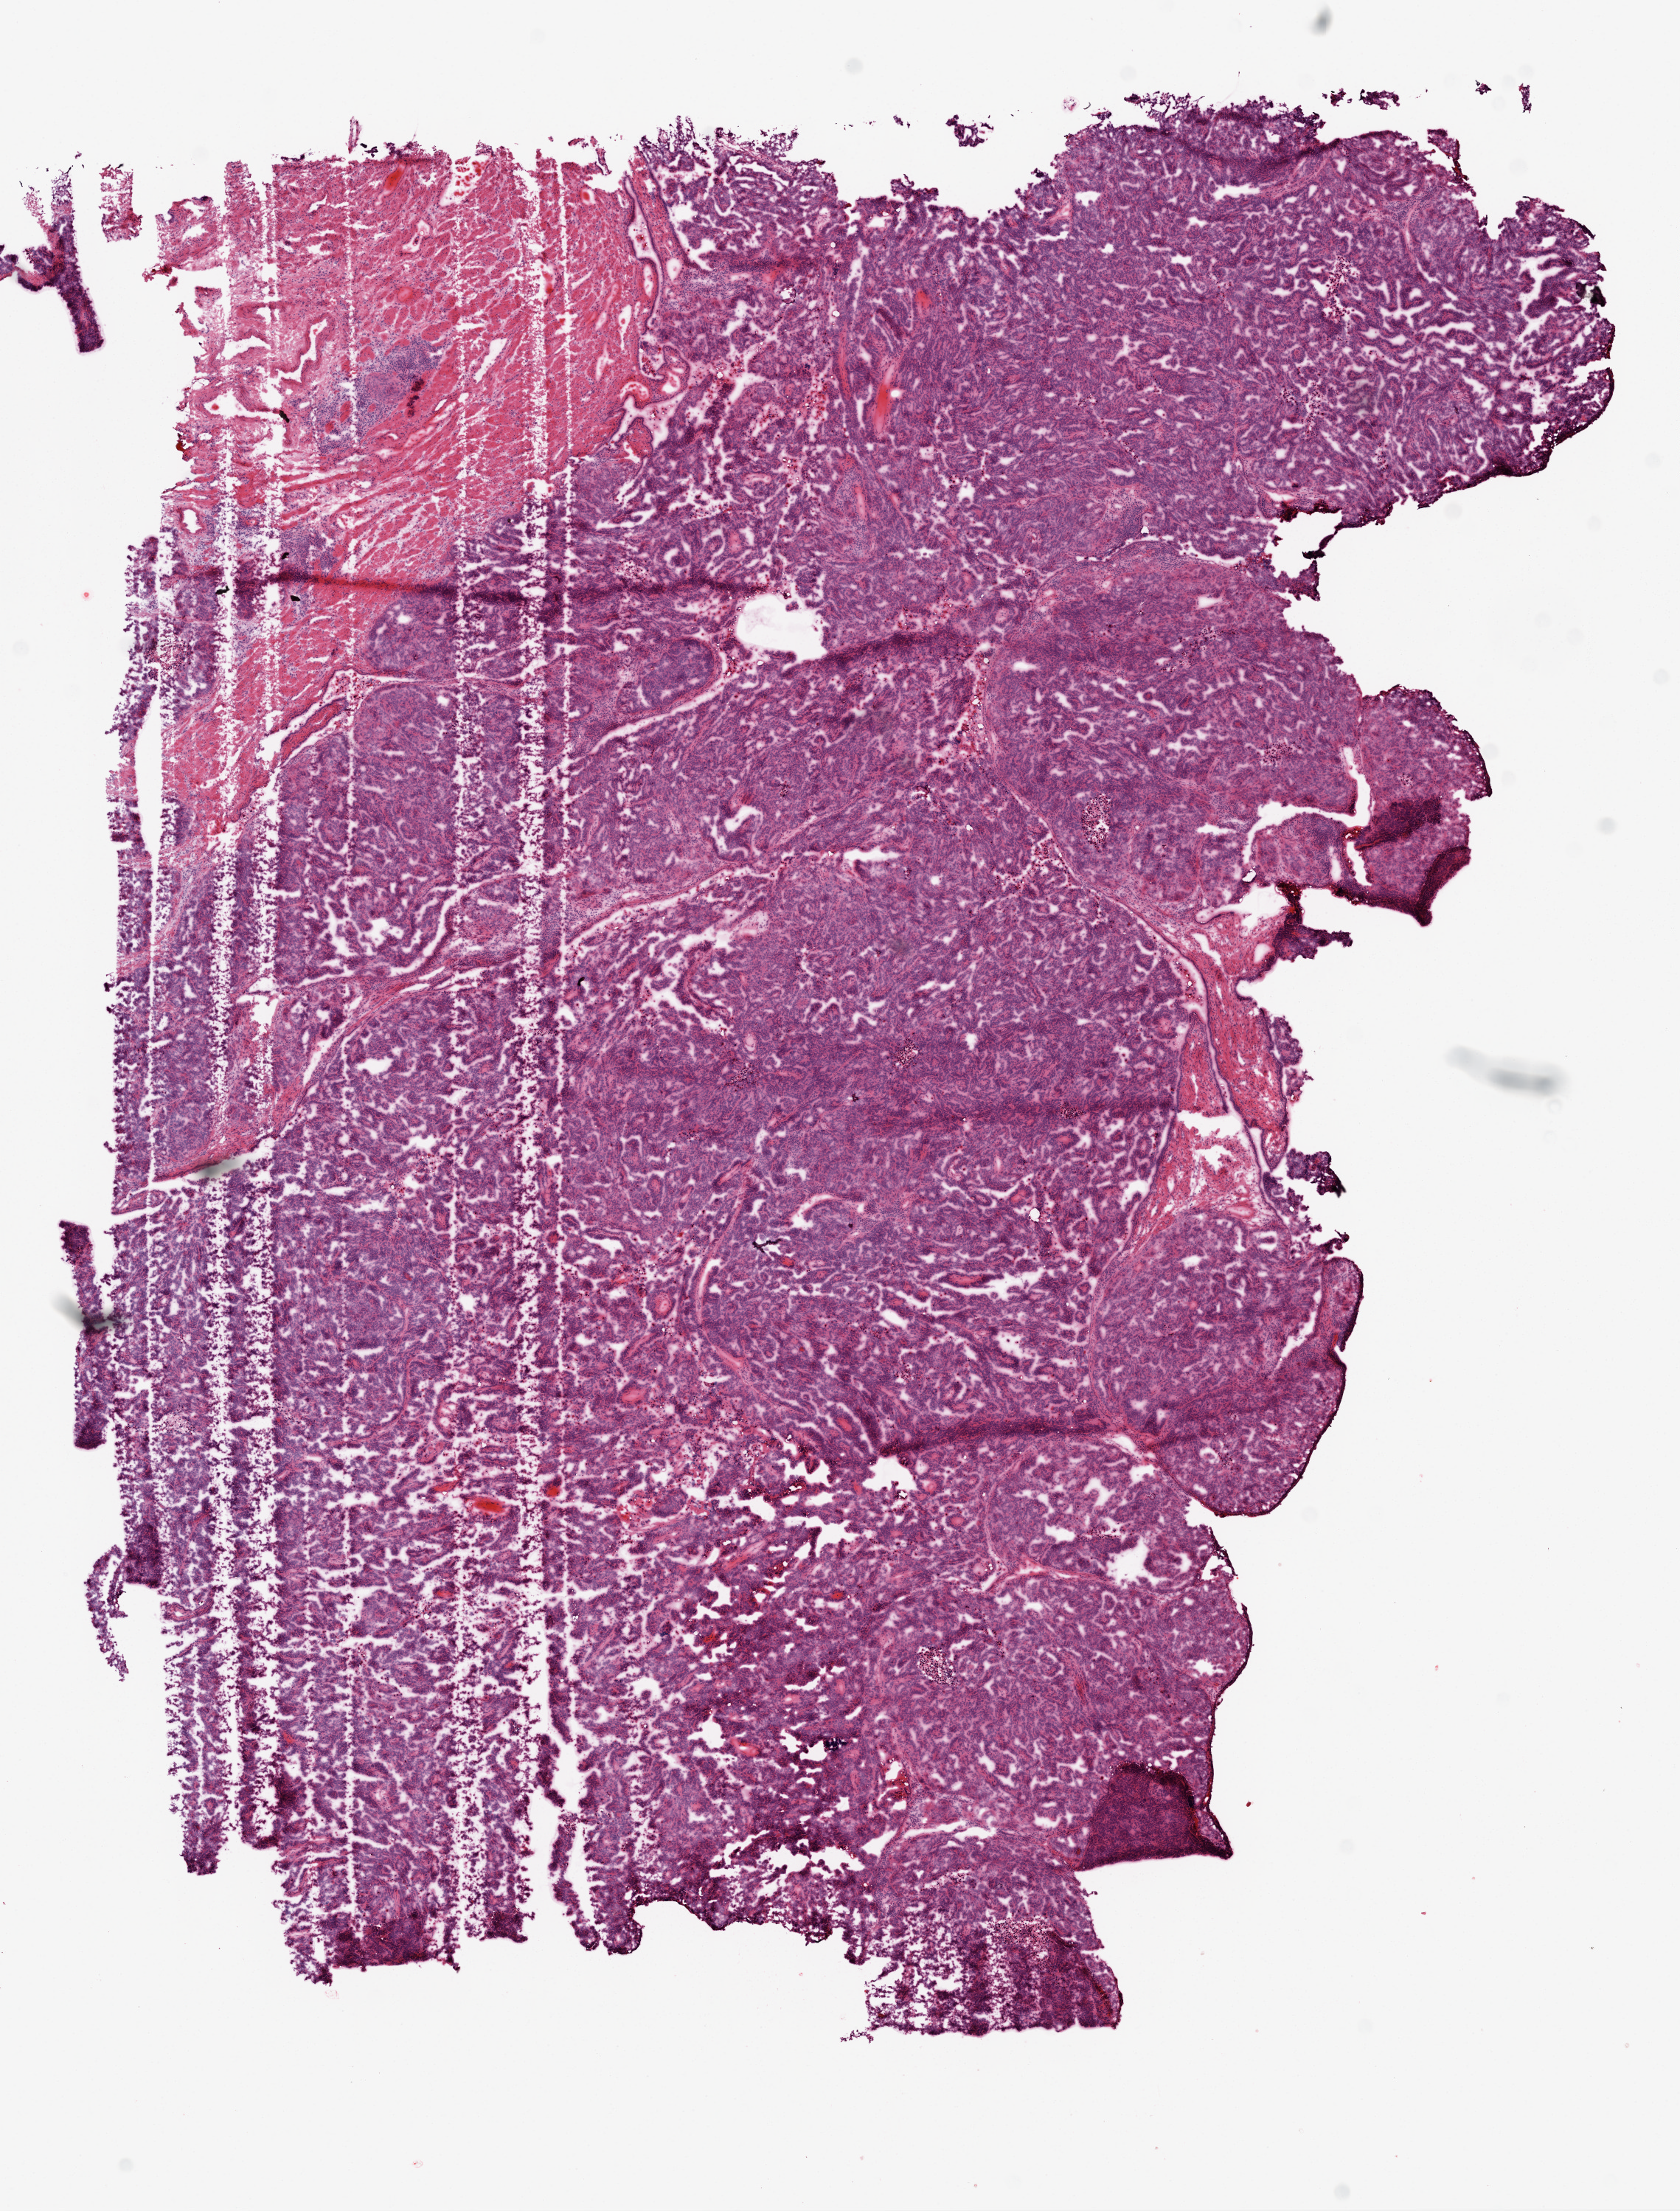
Whole-slide histology image, H&E — low-resolution overview of the scanned area, about 9.2 x 12.1 mm (from a 20x scan); frozen section from the top of the tissue portion; sample: primary tumour, ovary. Patient: female, age at initial diagnosis 74 years. Histologic grade: G3 (poorly differentiated). Slide review estimates, as recorded: tumour cells 90%, tumour nuclei 97%, normal cells 0%, stromal cells 10%, necrosis 0%.
FIGO stage: IIIC. Laterality: bilateral. Histologic diagnosis: Serous cystadenocarcinoma, NOS.